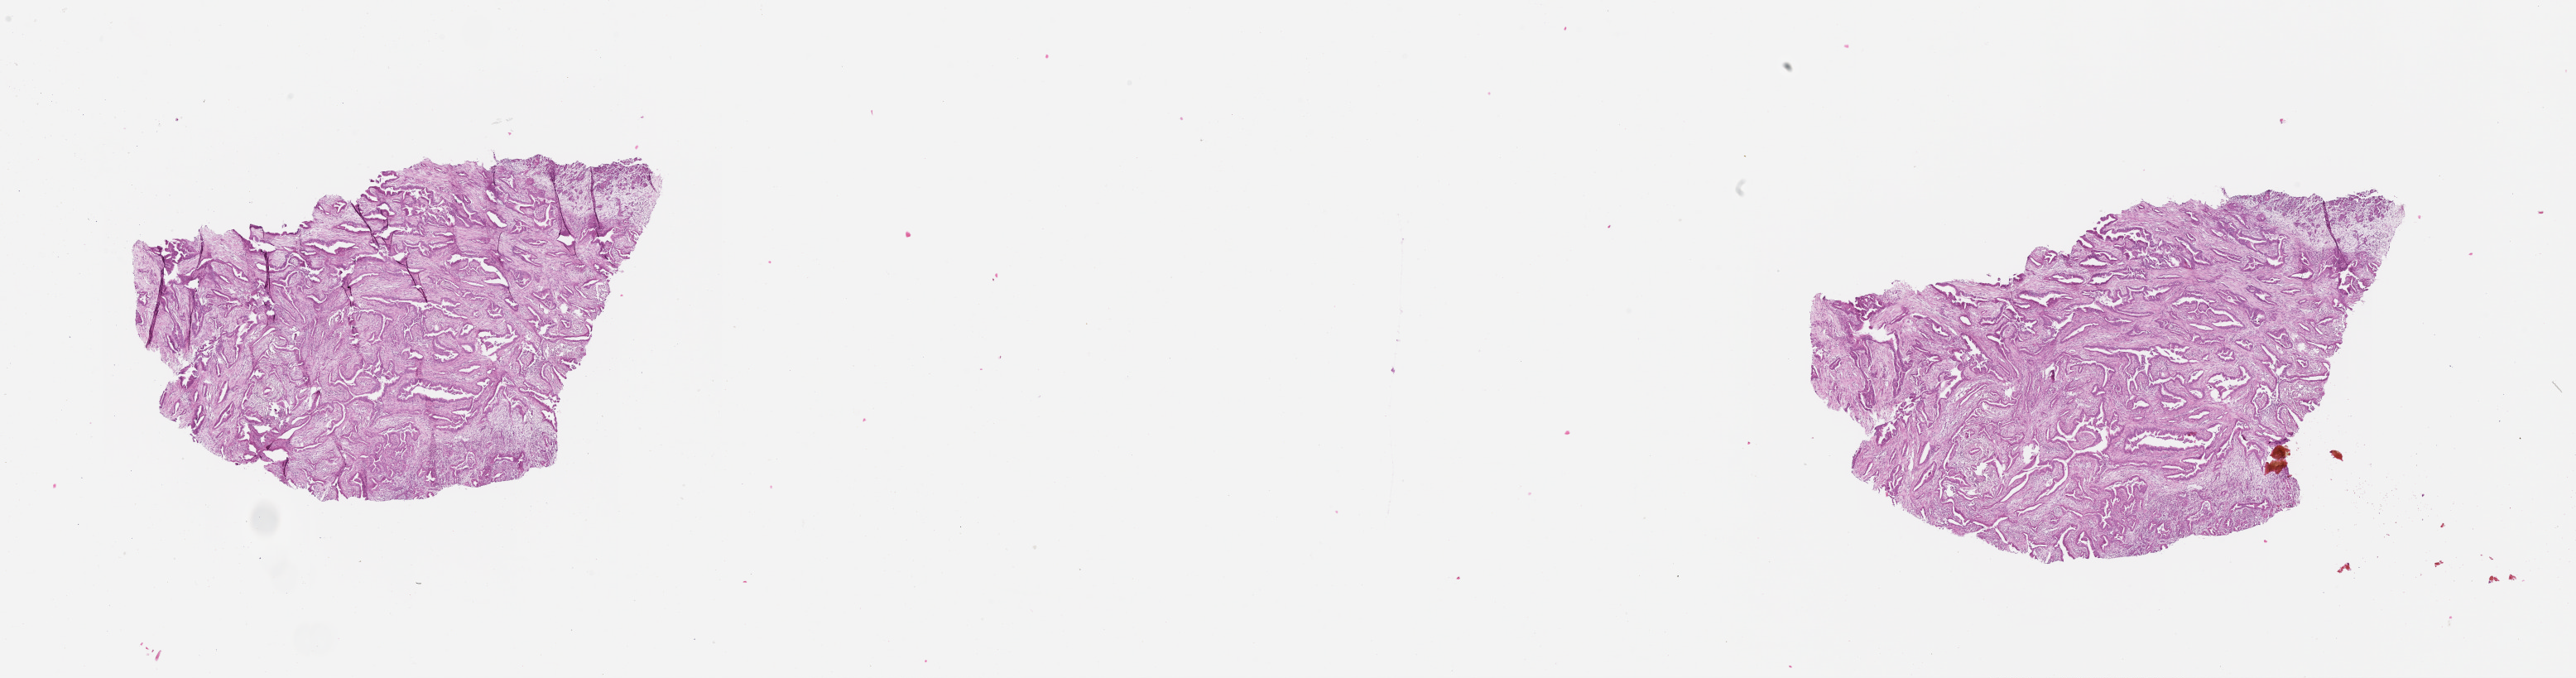
H&E whole-slide image — shown as a low-resolution overview of the whole scanned area (about 25.1 x 6.6 mm, acquisition: 20x scan). Tumour tissue sample, sampled site: pancreas. Male, 44 y/o. Histologic grade: G2 (moderately differentiated). Pathologist review of this section (percent, as recorded): tumour nuclei 30%, necrosis 0%.
- AJCC pathologic stage: III
- histologic diagnosis: Infiltrating duct carcinoma, NOS
- primary tumour site (as recorded): head